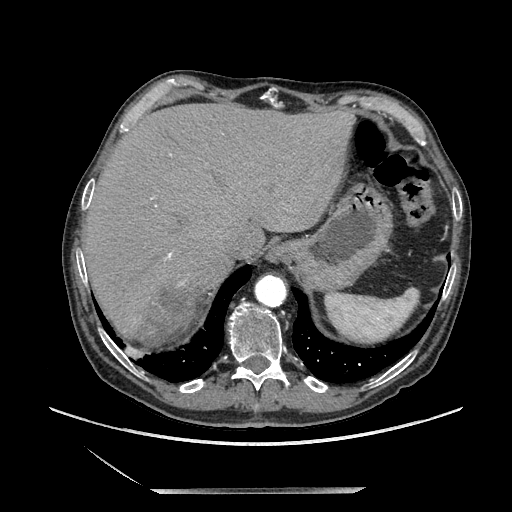
Contrast-enhanced abdominal CT, one axial slice. Soft-tissue window (W 400 / L 40 HU). 1.25 mm slice thickness. 512 × 512 image matrix, field of view 420 × 420 mm. Male patient. Case-level facts recorded for this patient, not image findings: diagnosis: adrenocortical carcinoma; tumour side: right adrenal; tumour size at pathology: 16 cm; Ki-67 index: 17 %; stage (as recorded): 3.
Structures marked on this image (semi-automatic segmentation, software-assisted and operator-edited):
- mass: bounding box <135,288,203,349> (left, top, right, bottom; pixels)